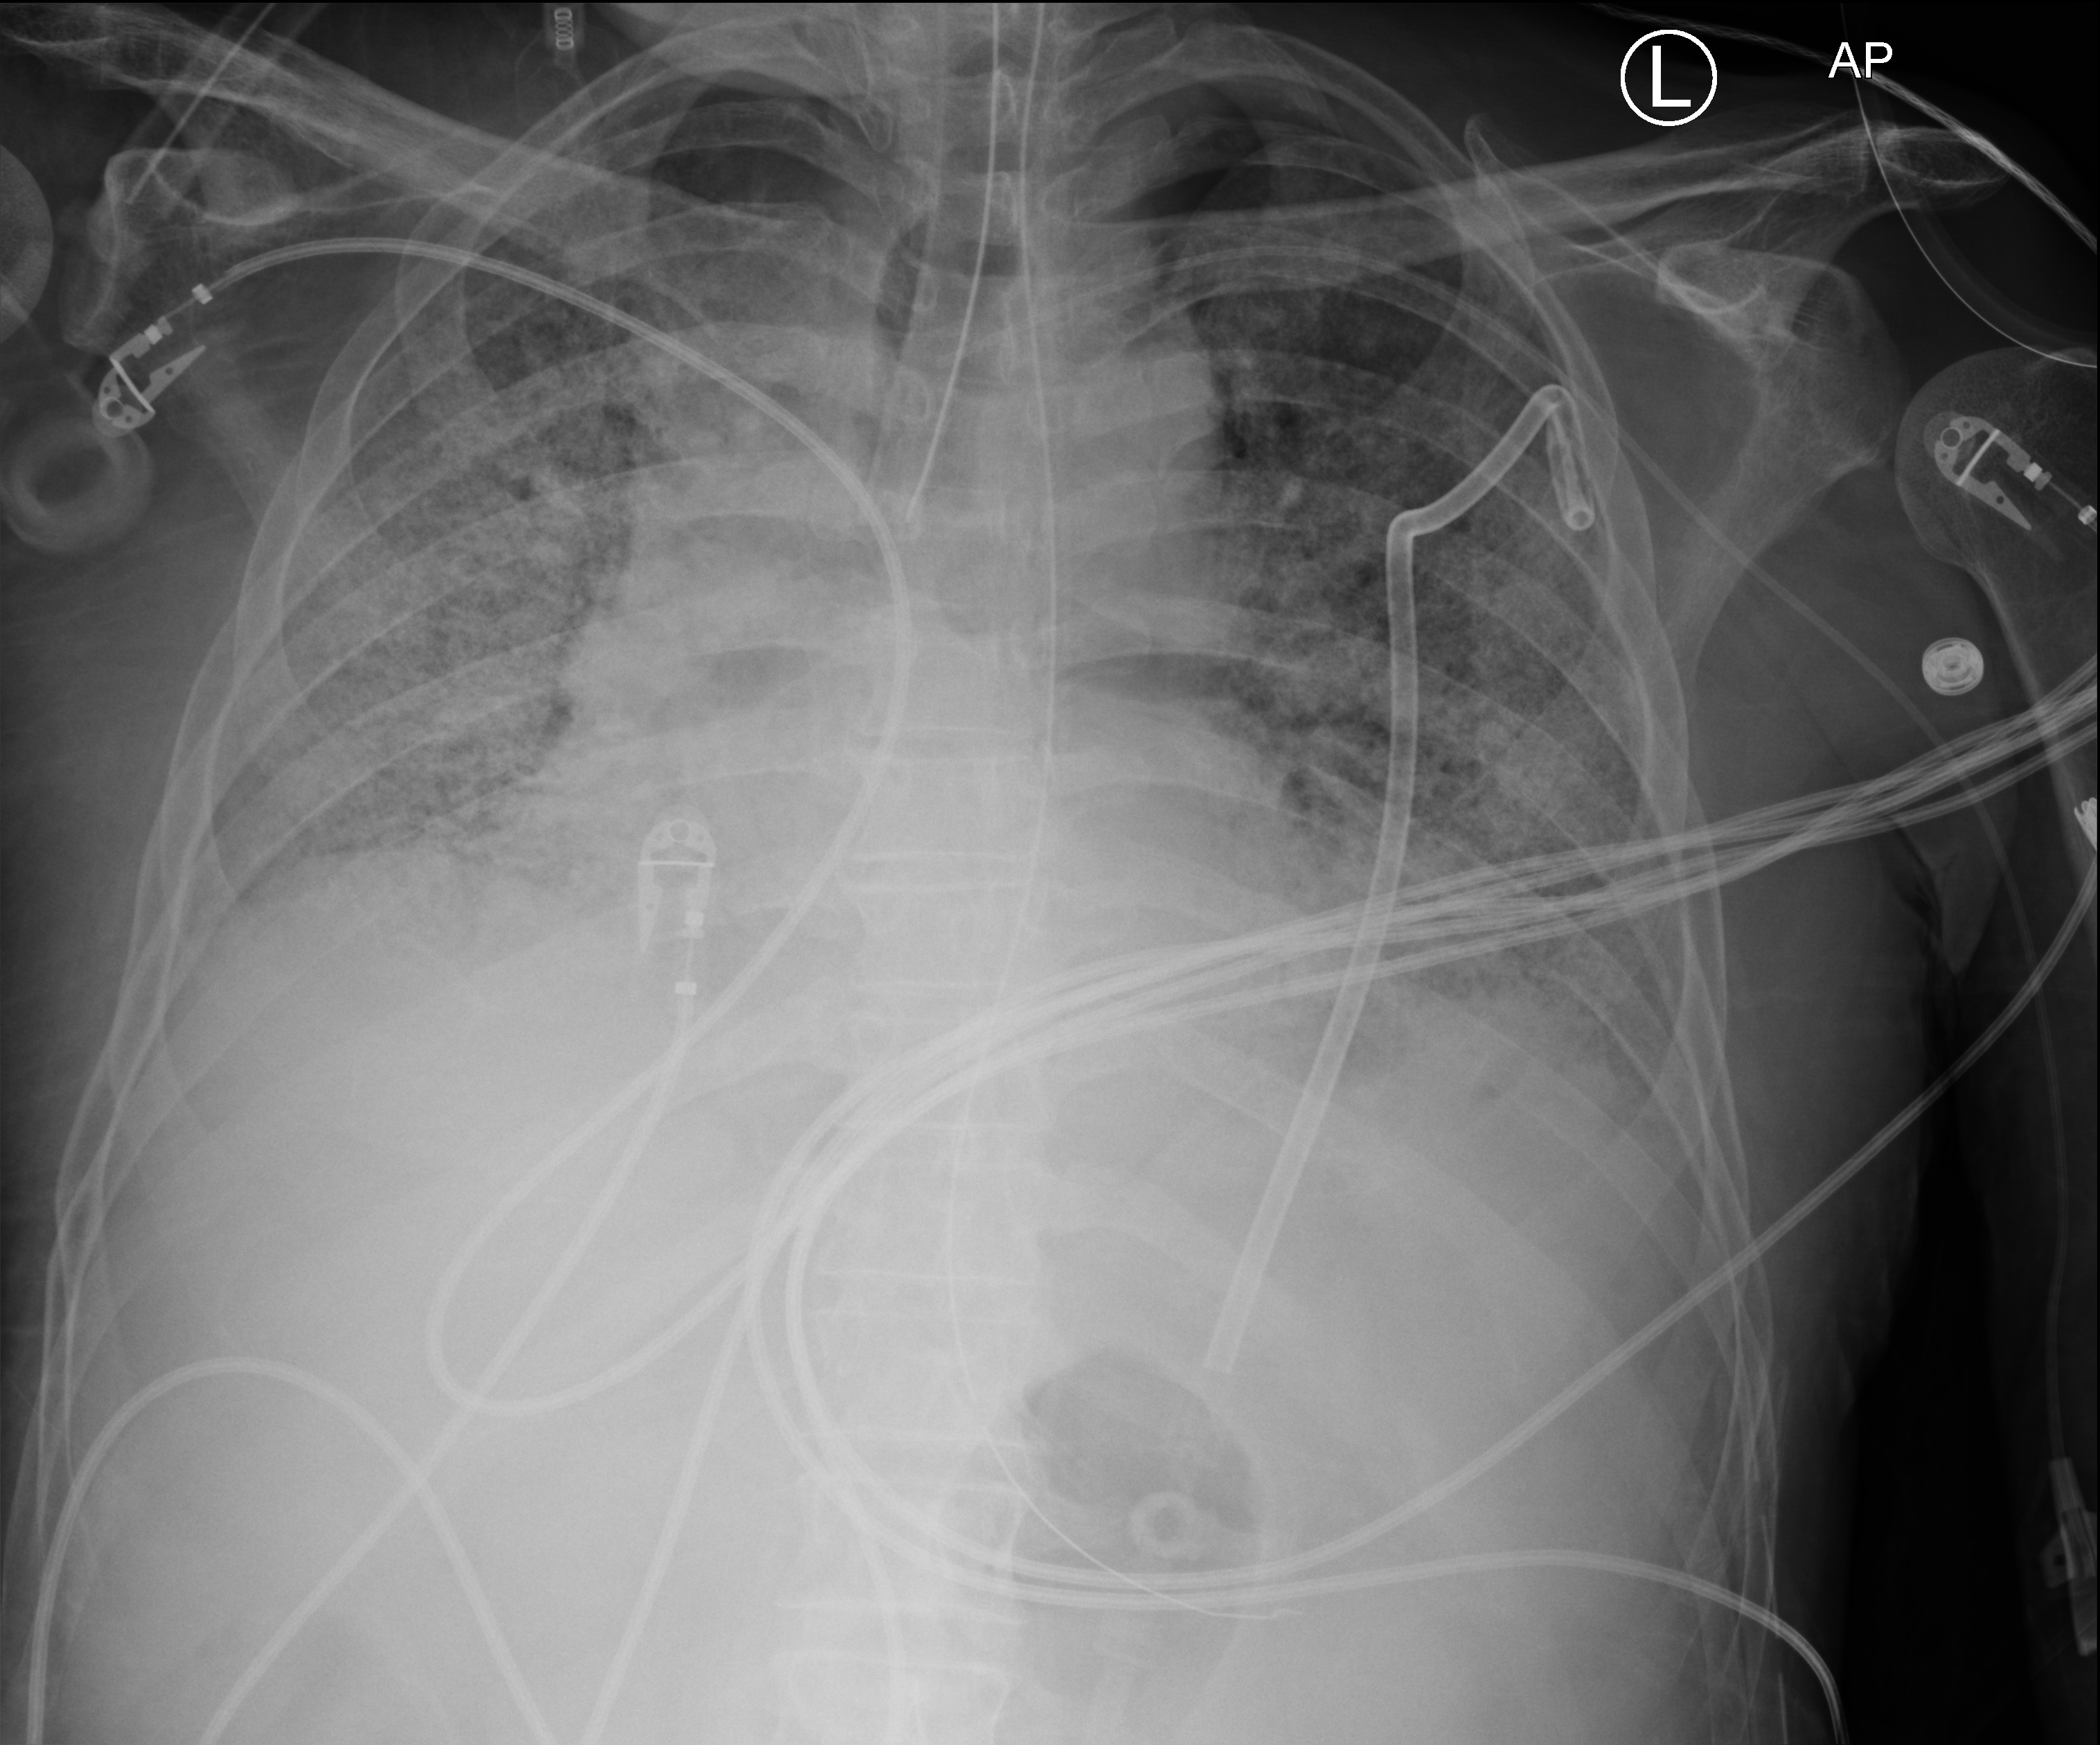
Bedside chest radiograph (computed radiography); anteroposterior (AP) projection. Male patient hospitalised with COVID-19, age 60–74 years.
Hospital-stay facts (about this admission, not read from this image; timing relative to this image not recorded):
- admitted to intensive care during this hospital stay: yes
- mechanically ventilated during this hospital stay: yes